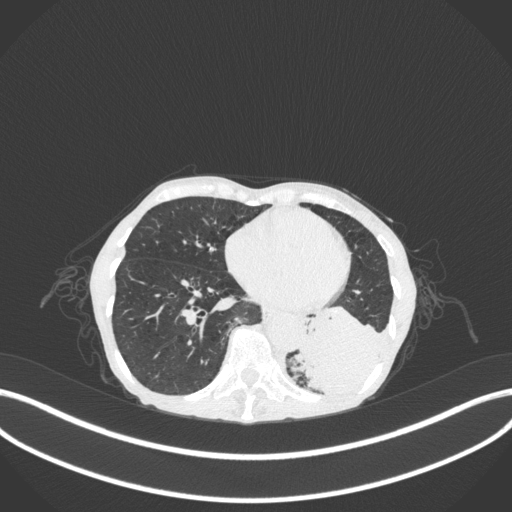
Chest CT, one axial slice. Slice 88 of 347 in the series (ordered by position). Lung window (W 1500 / L -600 HU). 1 mm slice thickness. 512 × 512 image matrix. Female patient, age 70 years. Case-level facts recorded for this patient, not image findings: clinical TNM (as recorded): T3 N0 M0.
Annotated regions visible in this slice (bounding box drawn by a radiologist):
- lung tumour (recorded histology: small cell carcinoma): box from (x=294, y=300) to (x=391, y=401) px